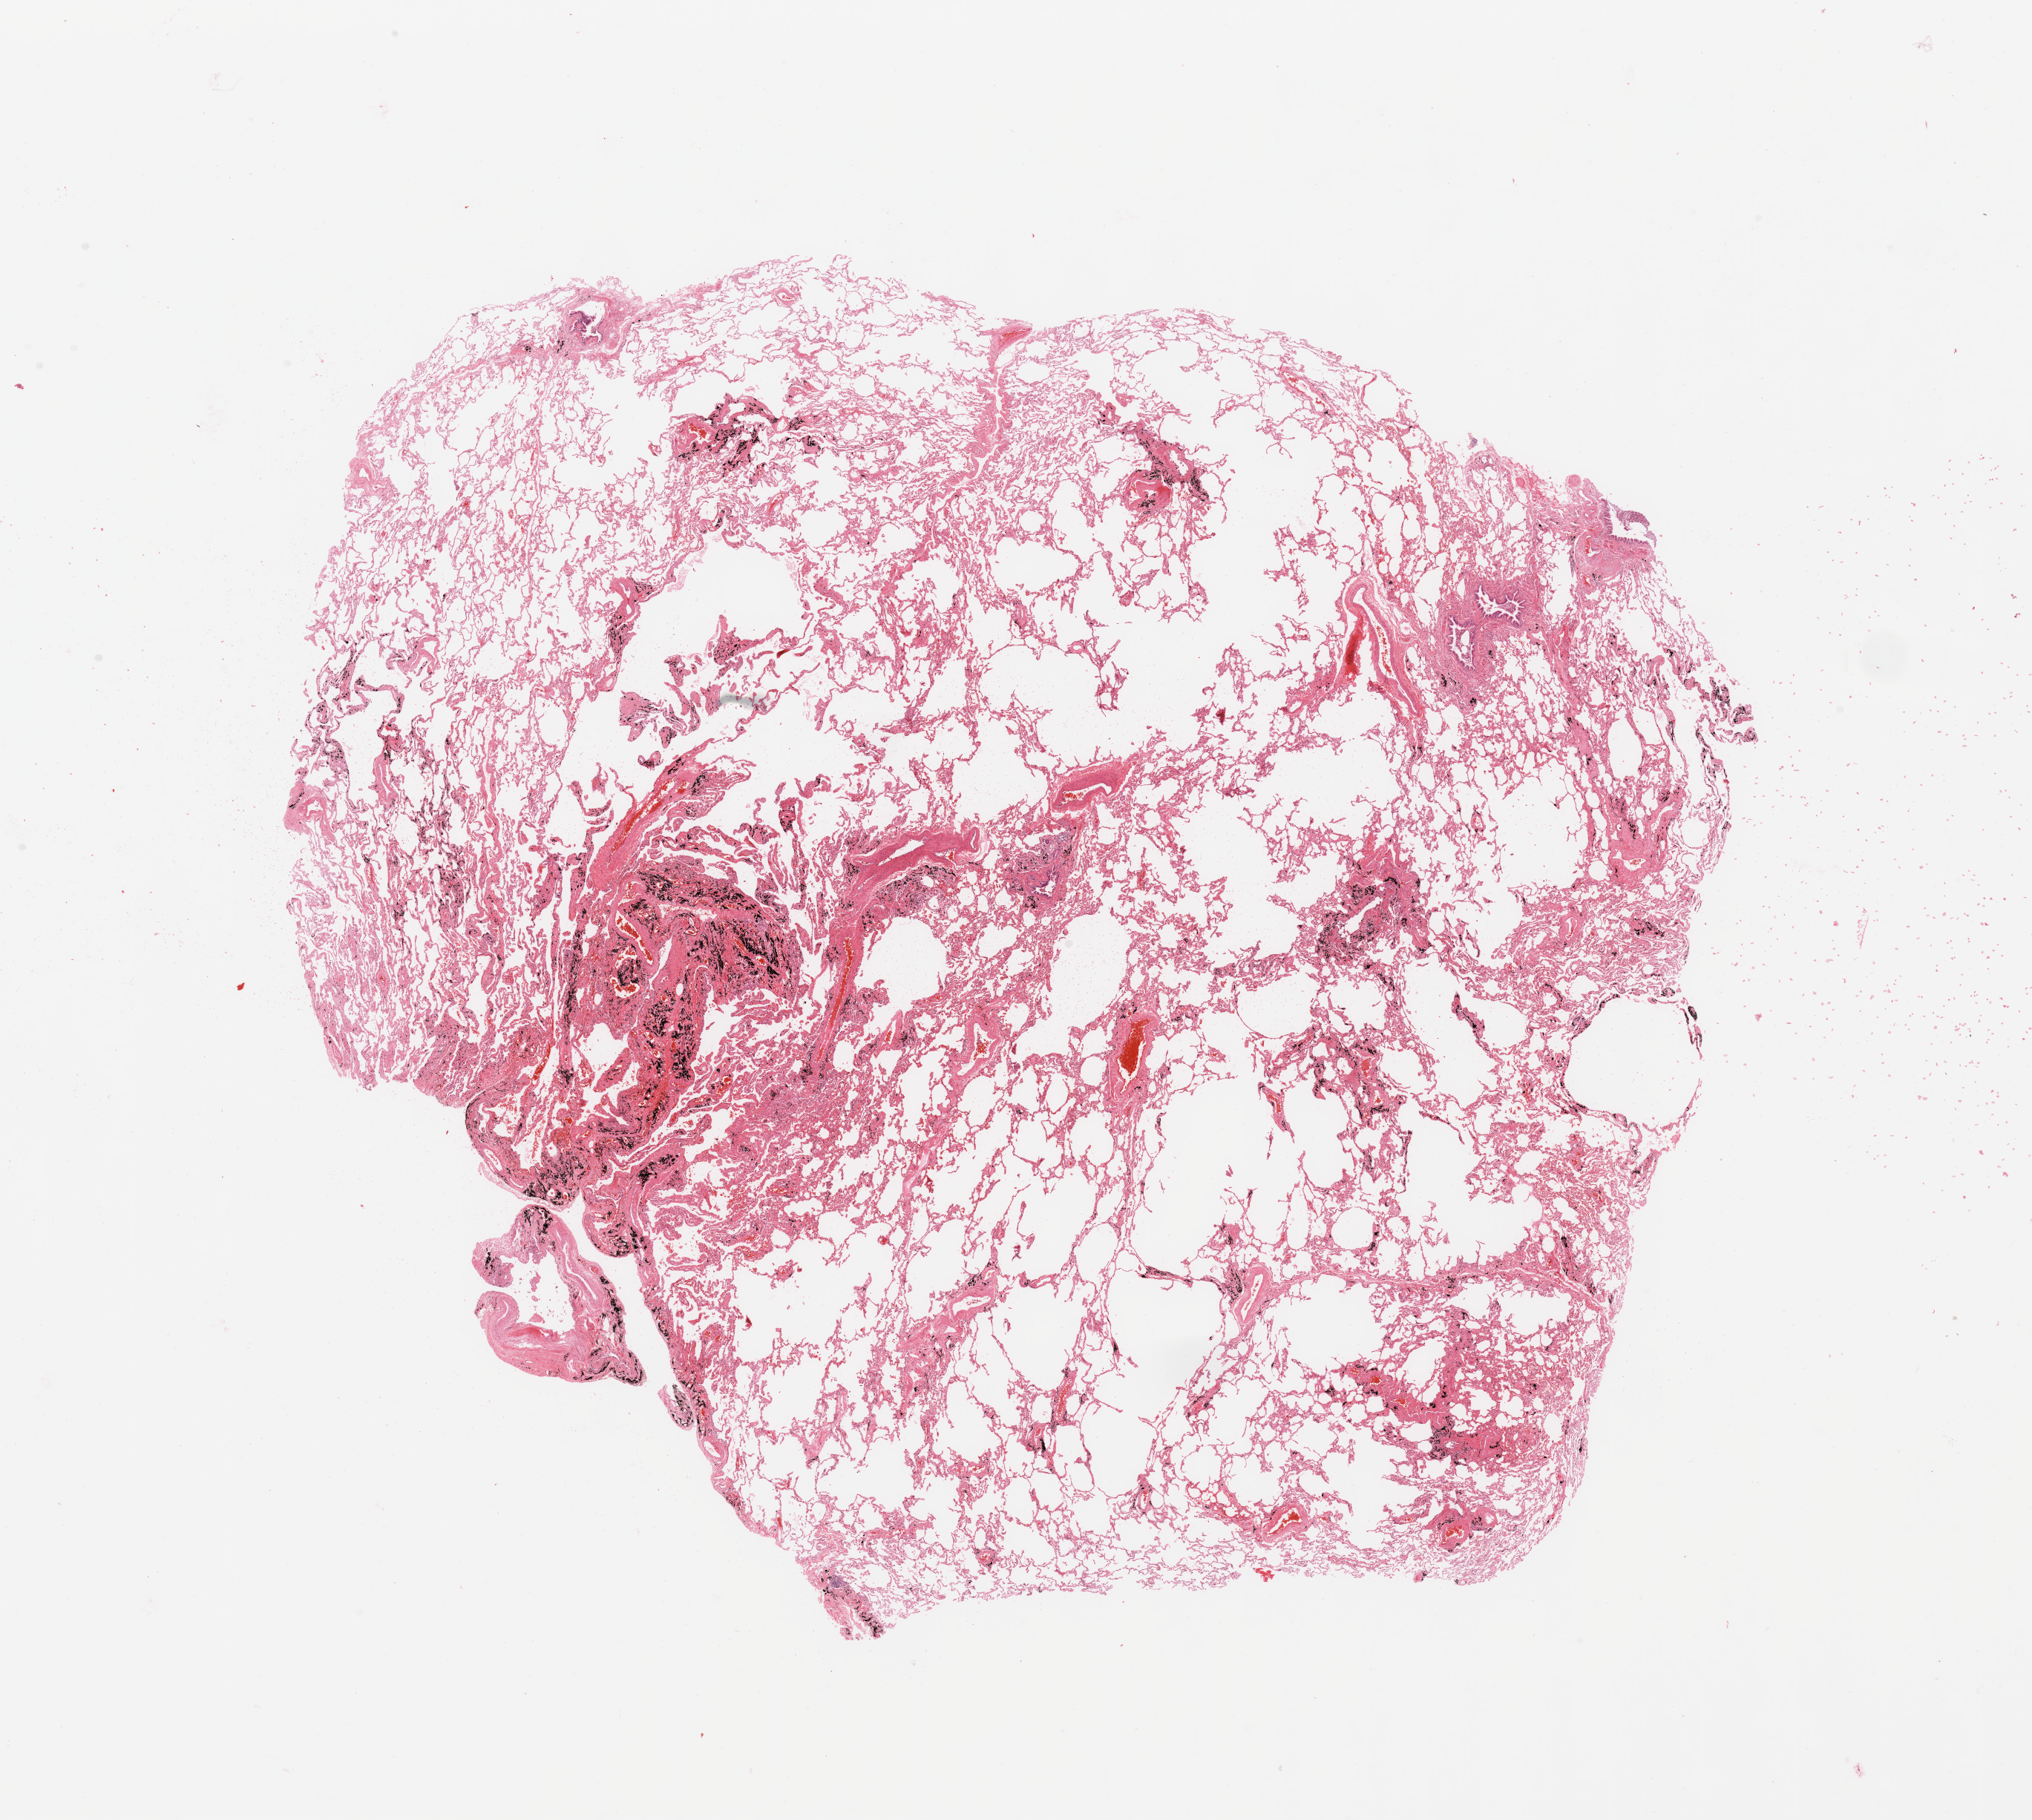
H&E-stained whole-slide image, low-resolution overview of the scanned area, about 21.7 x 19.4 mm (from a 20x scan). Normal (non-tumour) tissue sample, lung. Male, 72 y/o.
This section: normal (non-tumour) tissue from the same patient. Patient diagnosis: Adenocarcinoma, NOS.